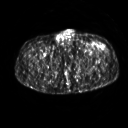
FDG PET of an extremity soft-tissue mass (from a PET/CT study), one axial slice. Position 259 of 267 along the scan axis. 3.27 mm slice thickness. 128 × 128 image matrix, field of view 500 × 500 mm. Patient: male, 64 years. From the clinical record (not read from this slice): histological type: extraskeletal osteosarcoma; grade: high; site of the primary tumour: thigh.
Annotated regions visible in this slice (expert contour drawn on MRI and transferred to this co-registered scan by the dataset authors):
- gross tumour volume (mass): bounding box (x1, y1, x2, y2) in pixels: (94, 42, 105, 48)